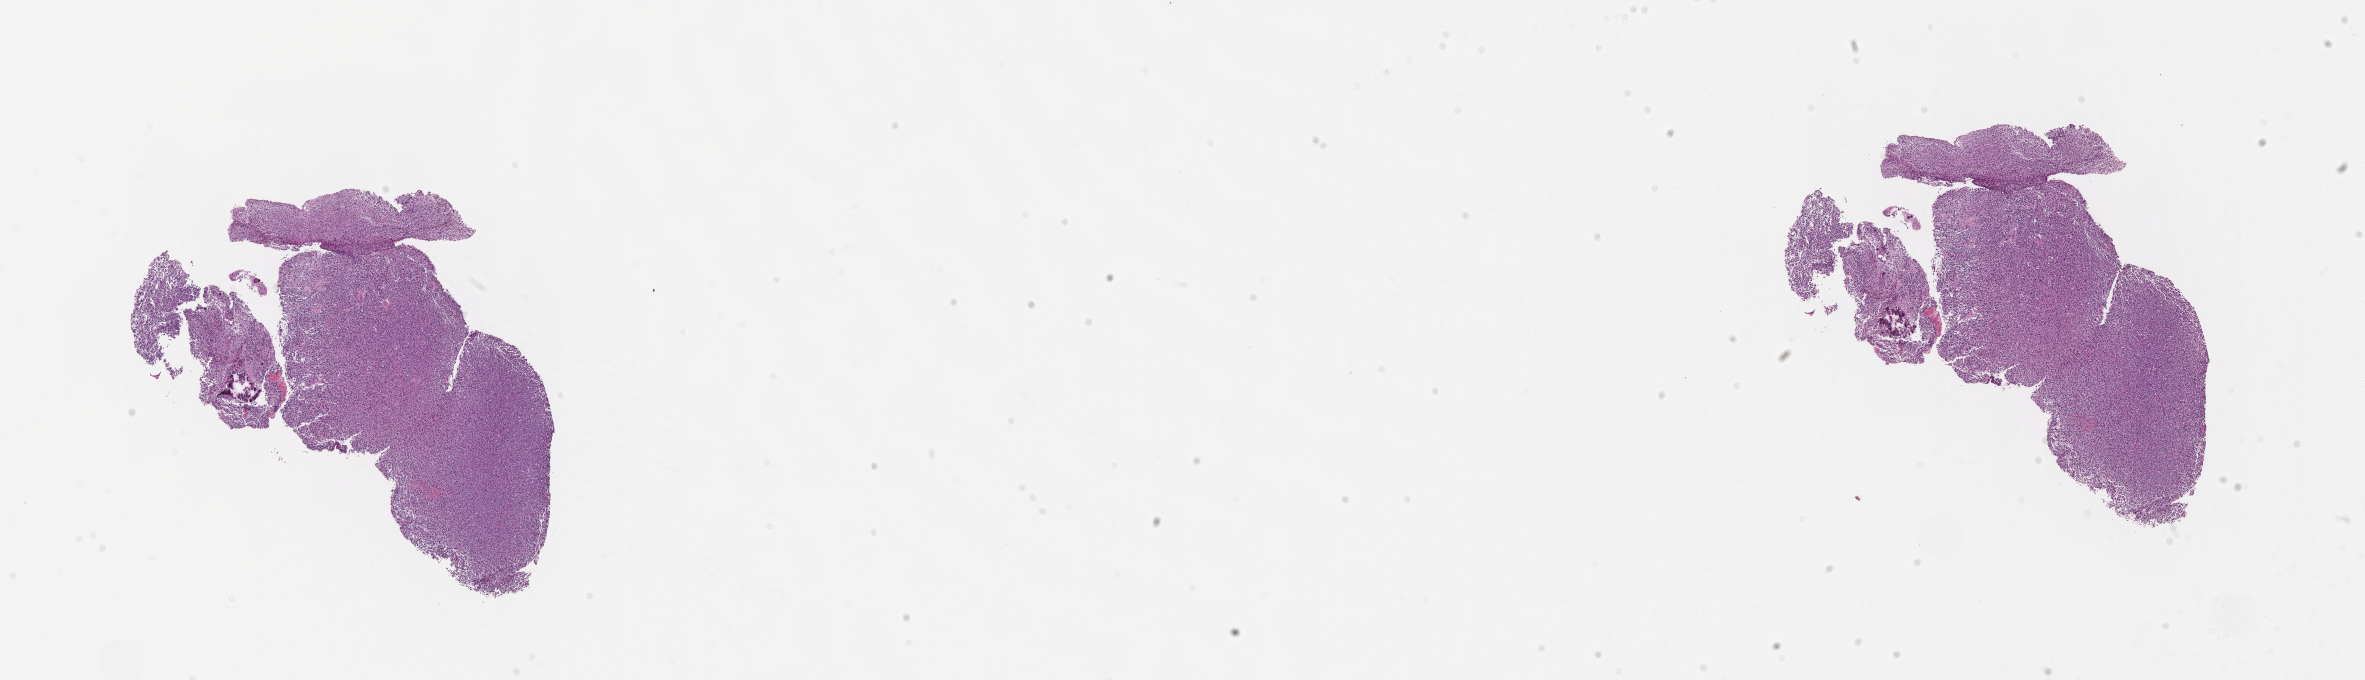
Digitized Hematoxylin and eosin (H&E) stained tissue section (whole slide) — whole scanned area (about 19.1 x 5.5 mm, acquisition: 40x scan) shown as a low-resolution overview; formalin-fixed paraffin-embedded (FFPE) diagnostic section; primary tumour sample from the brain. Female, age 74 years at initial diagnosis. Histologic grade: G3 (poorly differentiated).
* laterality: right
* pathologic diagnosis: Oligodendroglioma, anaplastic